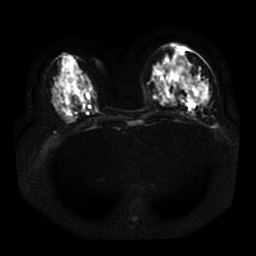
Breast MRI, one axial slice; slice 18 of 41 in the series (ordered by position); diffusion-weighted series; image 2 of 4 stored at this slice position (different b-values; order by instance number); 1.5 T; 5 mm slice thickness; 256 × 256 image matrix, field of view 330 × 330 mm. Female patient.
Outlined on this slice (outlined manually by an expert reader):
- tumour on diffusion-weighted imaging: bounding box <170,59,207,102> (left, top, right, bottom; pixels)